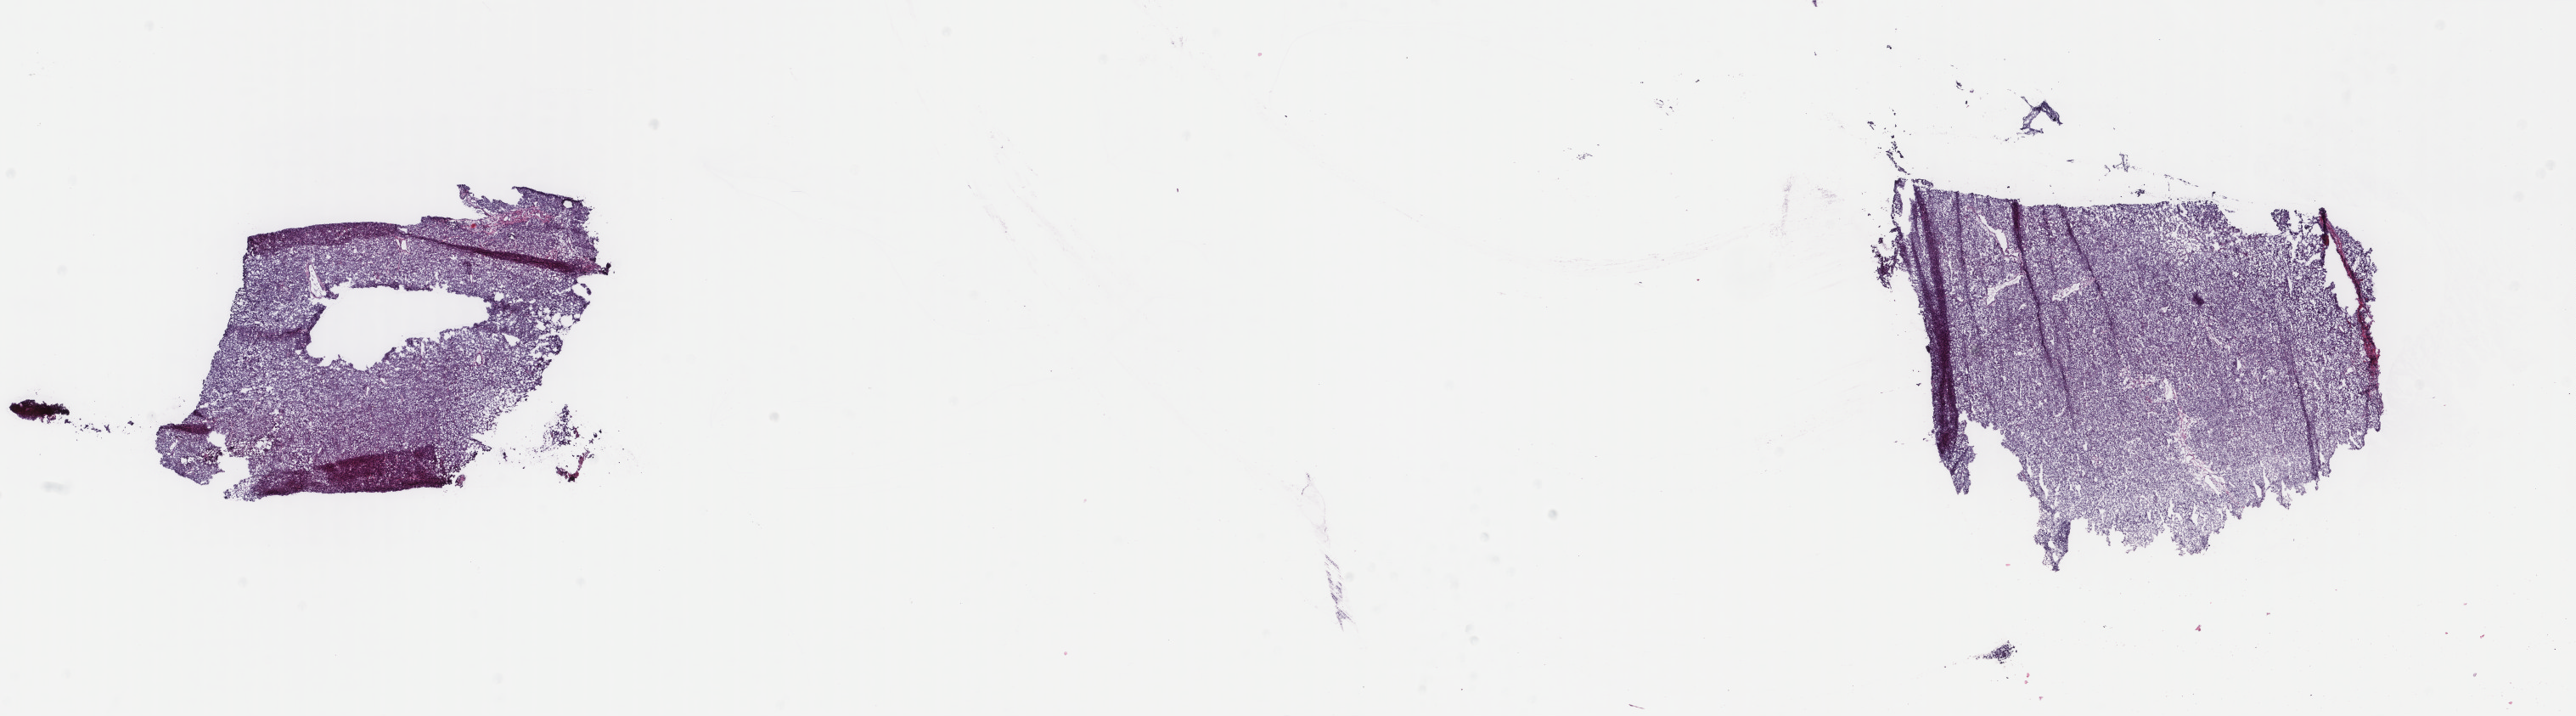
Whole-slide histology image, H&E — whole scanned area (about 24.1 x 6.7 mm, acquisition: 40x scan) shown as a low-resolution overview. Frozen section from the top of the tissue portion. Metastatic tumour sample. Female, age 55 years at initial diagnosis. Pathologist review of this section (percent, as recorded): tumour cells 95%, tumour nuclei 95%.
This section: metastatic tumour tissue. Patient diagnosis: Malignant melanoma, NOS.